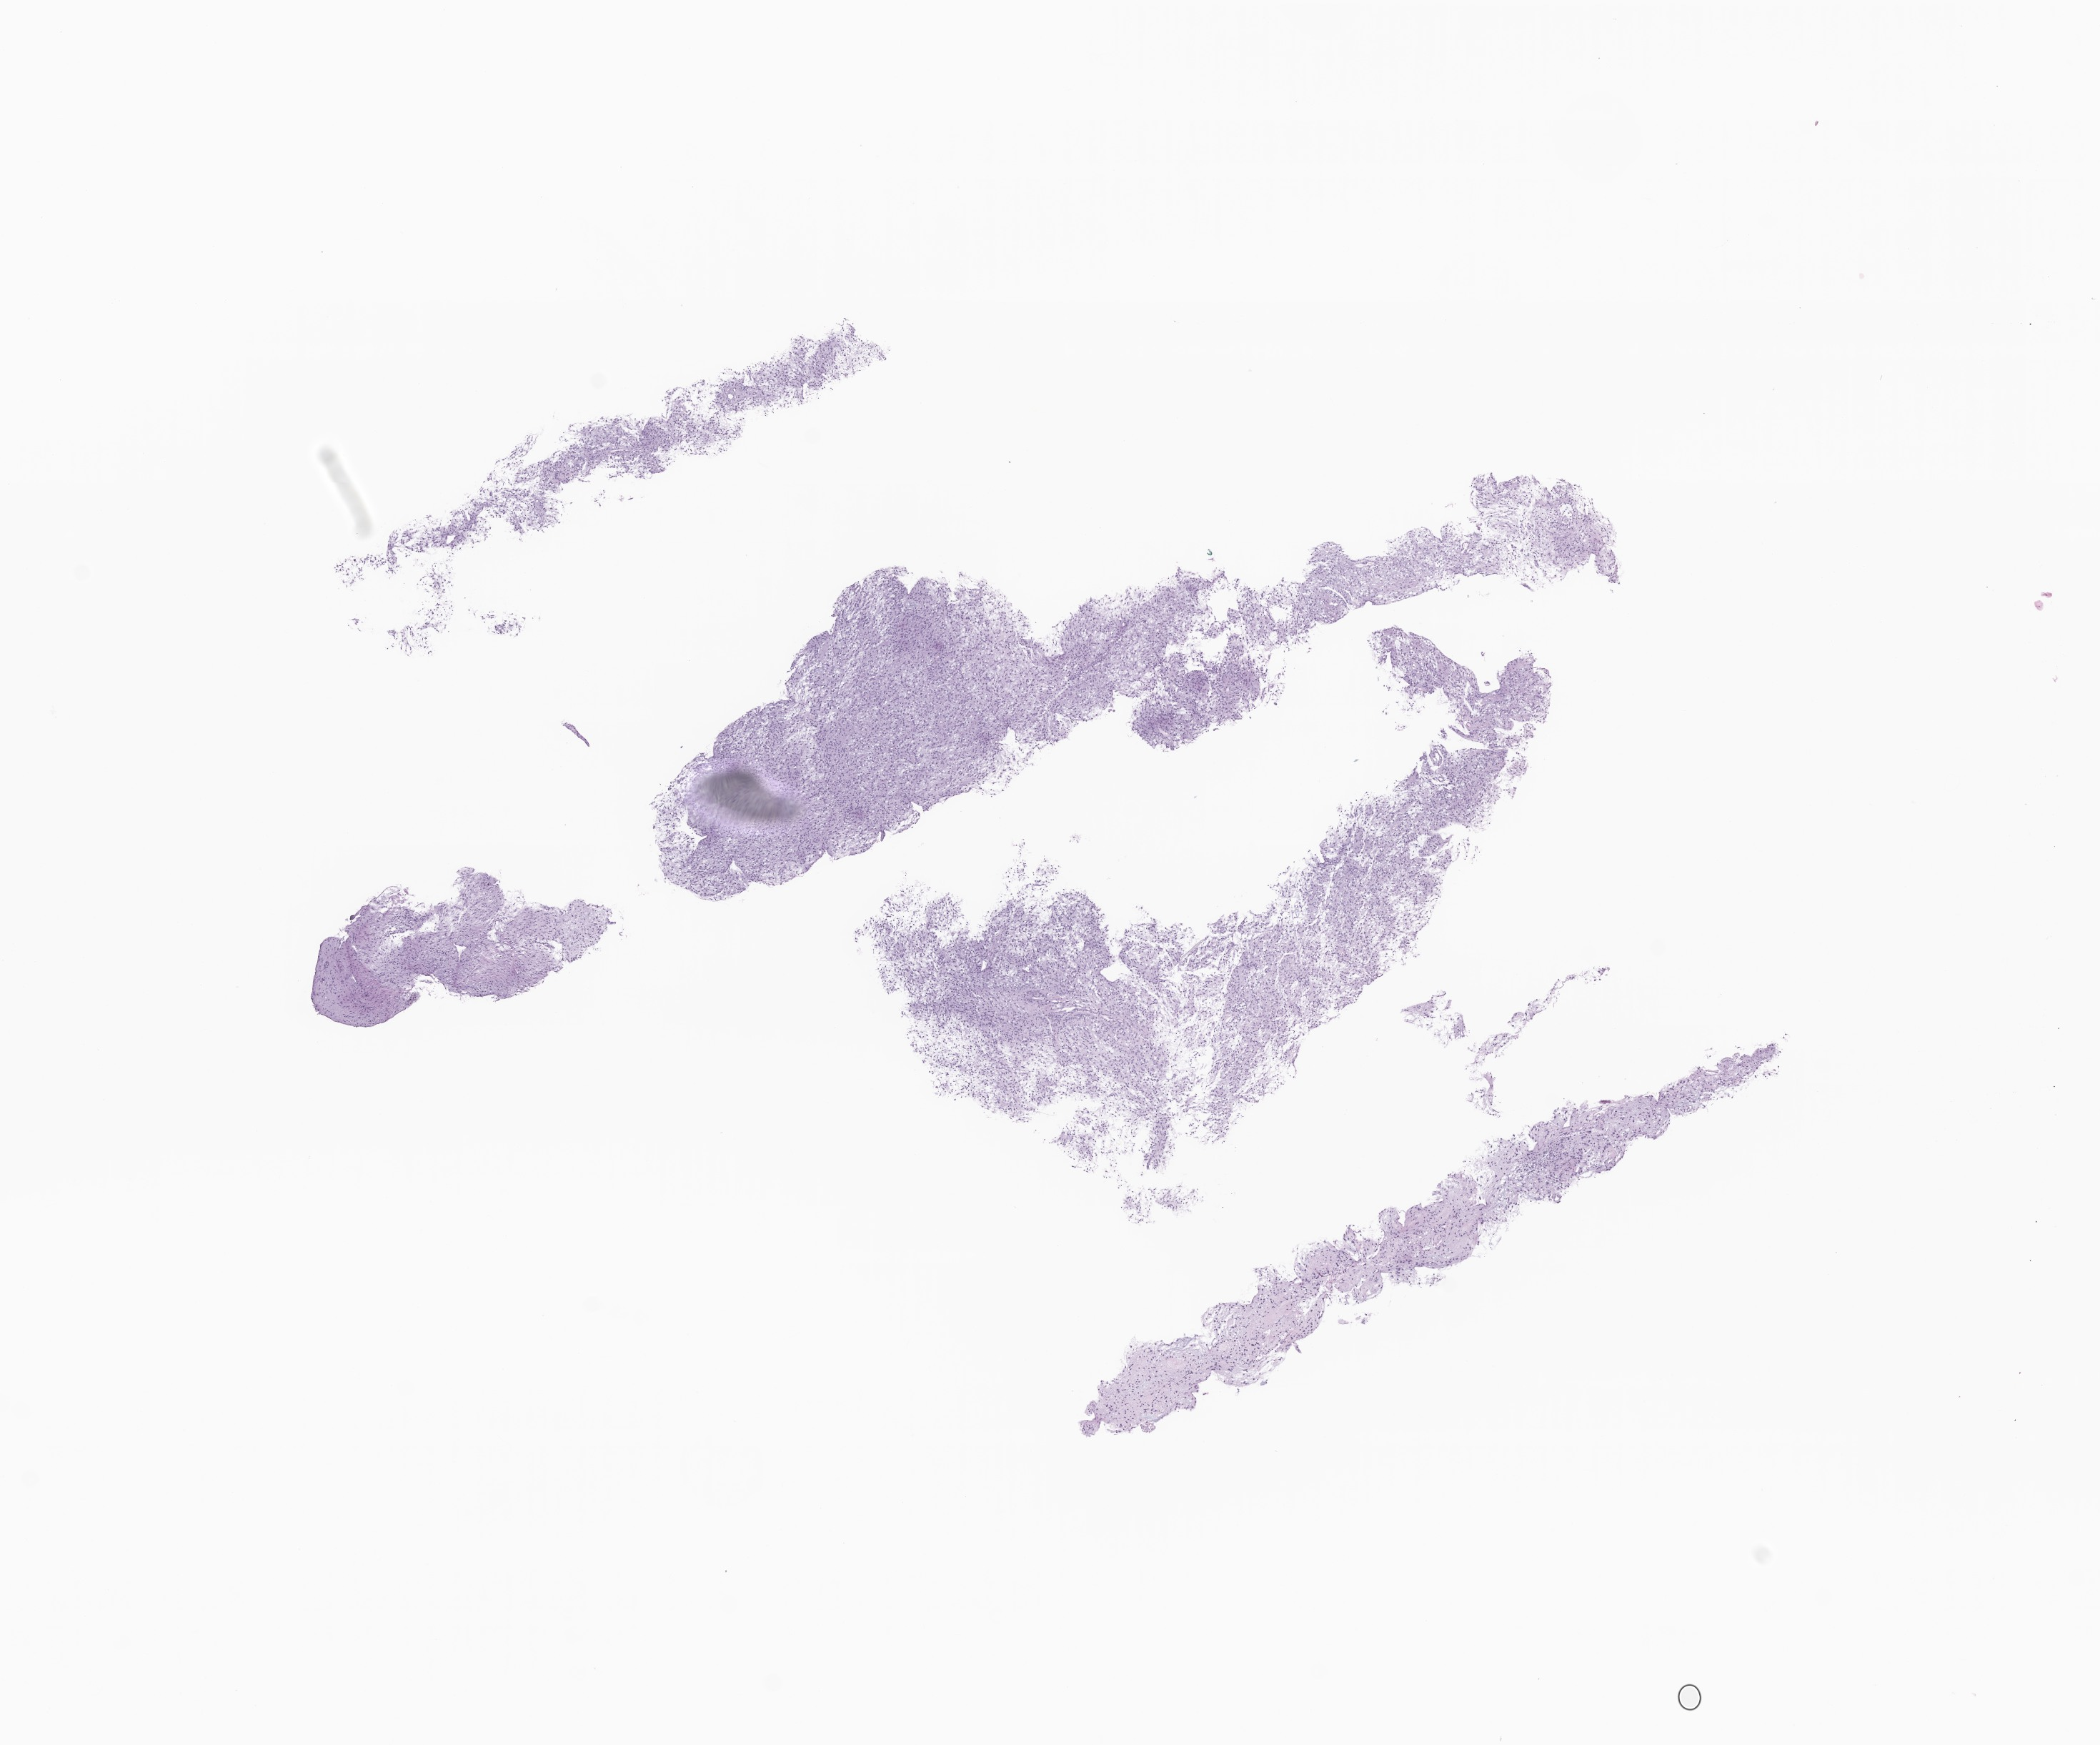
H&E whole-slide image of tumor tissue from the brain stem — shown as a low-resolution overview of the whole scanned area (about 12.4 x 10.3 mm). FFPE section. Patient: male, age 119 months (9 years 11 months).
Diagnosis: Pilocytic astrocytoma.